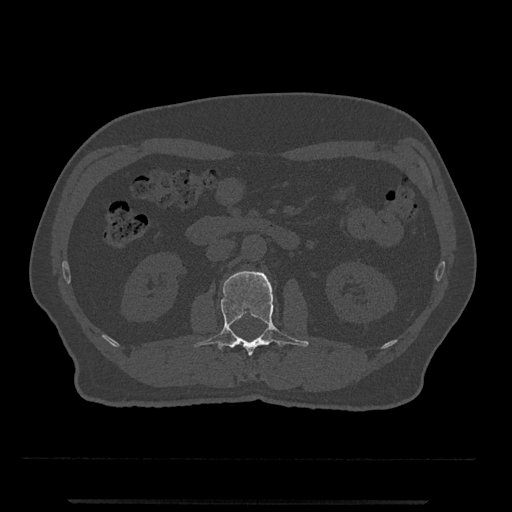
CT including the spine, one axial slice. Slice 269 of 797 in the series (ordered by position). Reconstruction kernel Br40s/3. Bone window (W 1800 / L 400 HU). 512 × 512 image matrix. Male patient, age 63 years. From the clinical record (not read from this slice): primary cancer: prostate.
Structures marked on this image (semi-automatic segmentation, software-assisted and operator-edited):
- L2 vertebra: box from (x=194, y=271) to (x=309, y=356) px